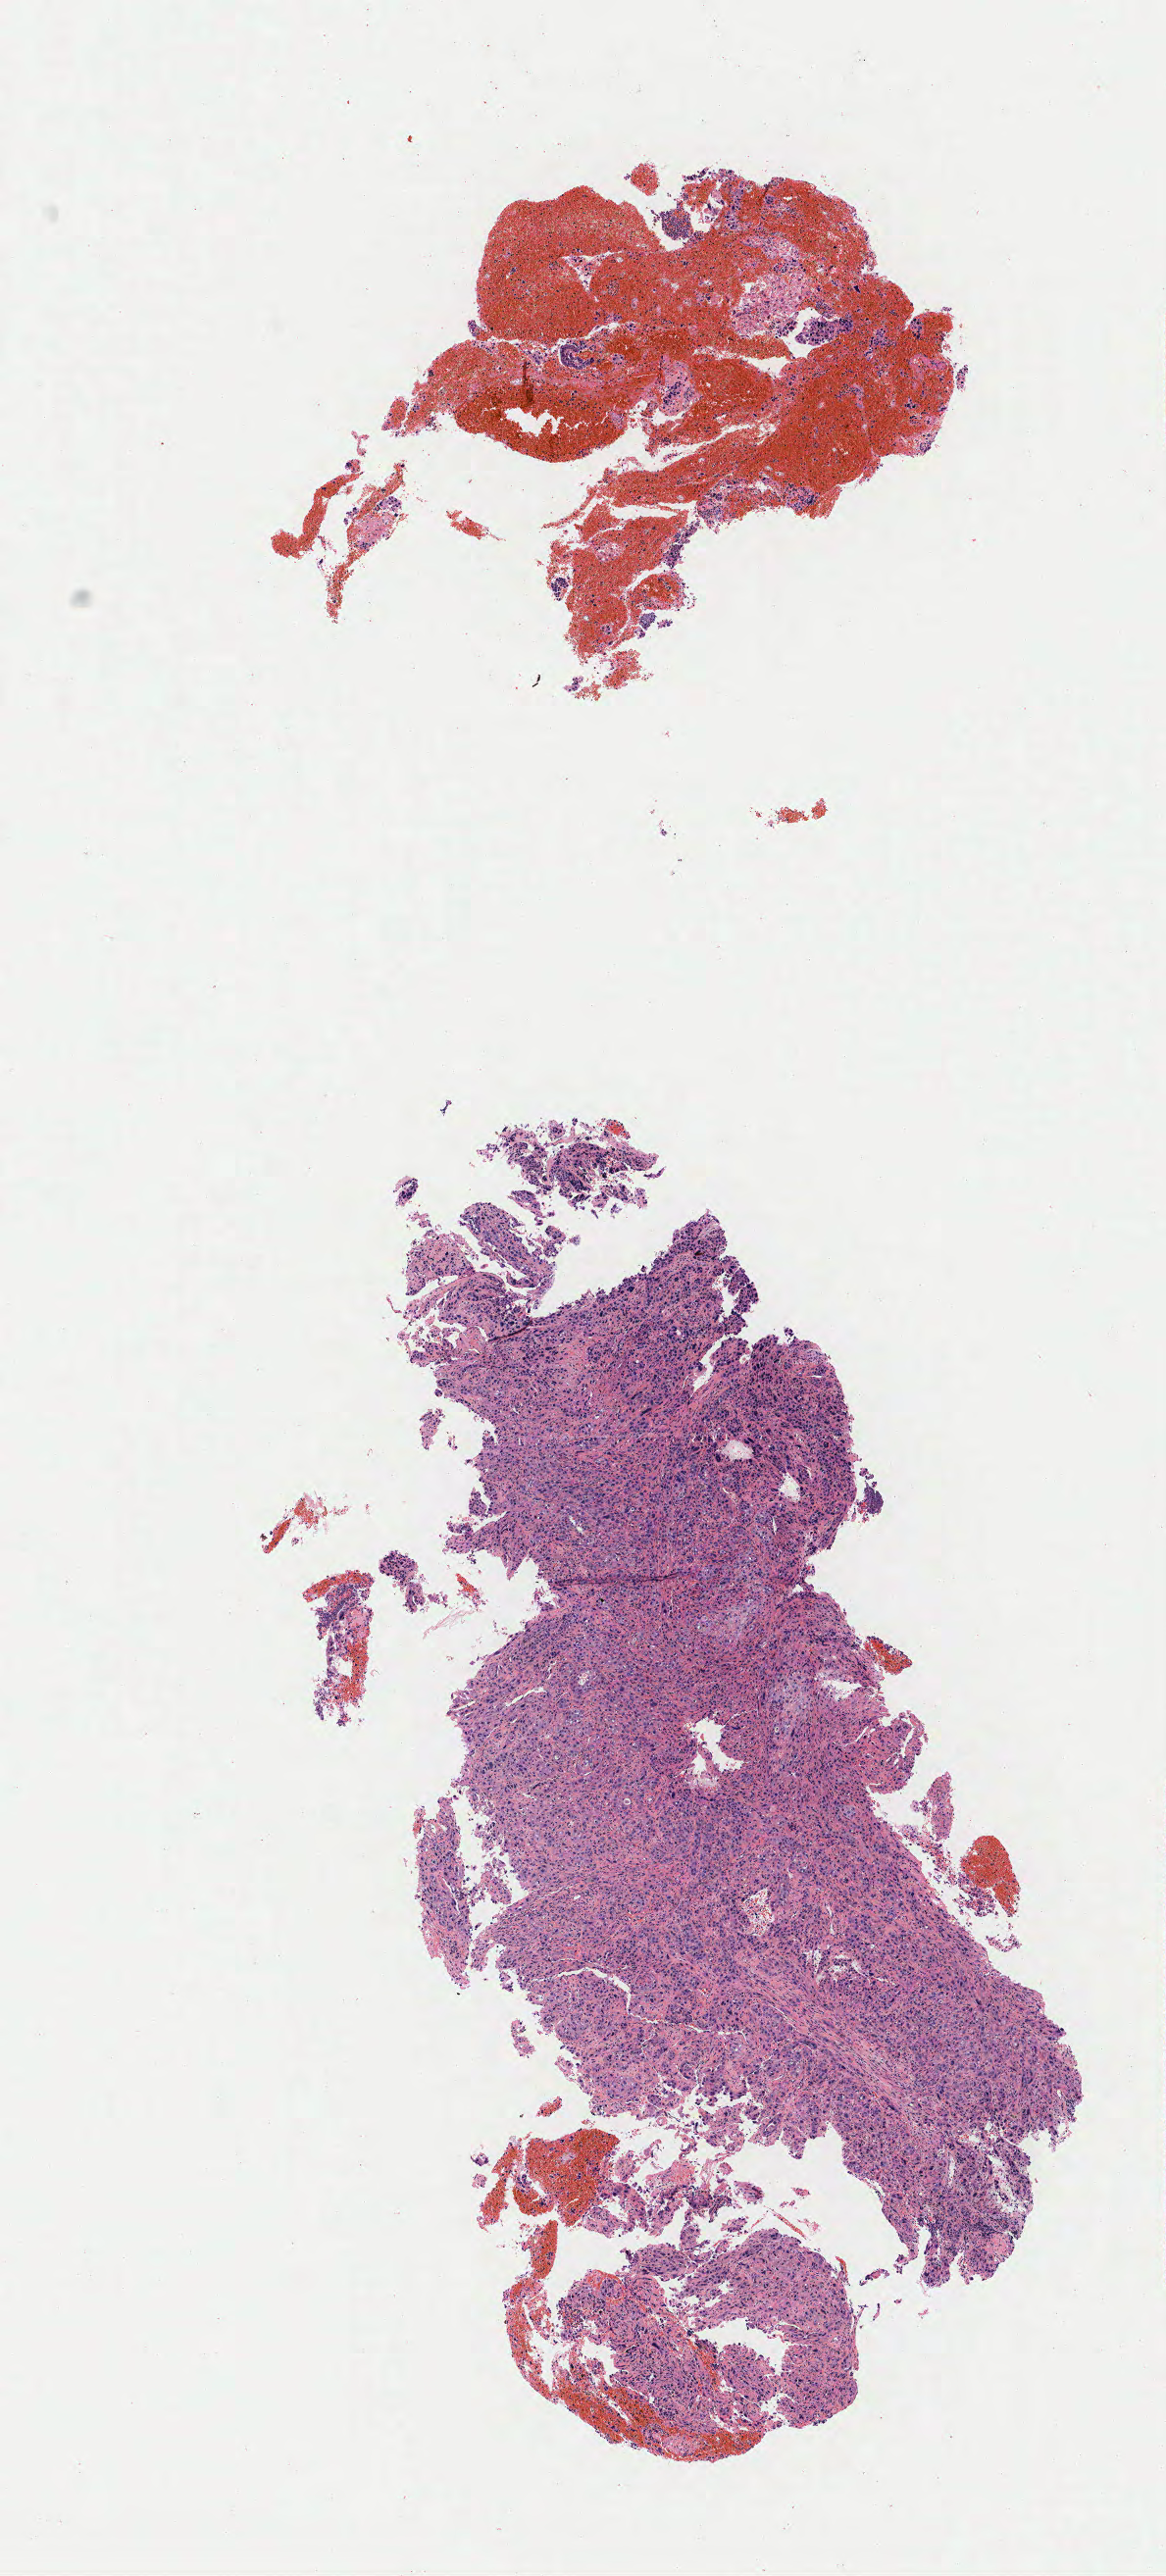
Digitized hematoxylin and eosin (H&E)-stained section — shown as a low-resolution overview of the whole scanned area (about 4.7 x 10.4 mm), specimen: tumor tissue, site: cervix. Patient: female, age 42 years.
* diagnosis: Squamous cell carcinoma, keratinizing, NOS